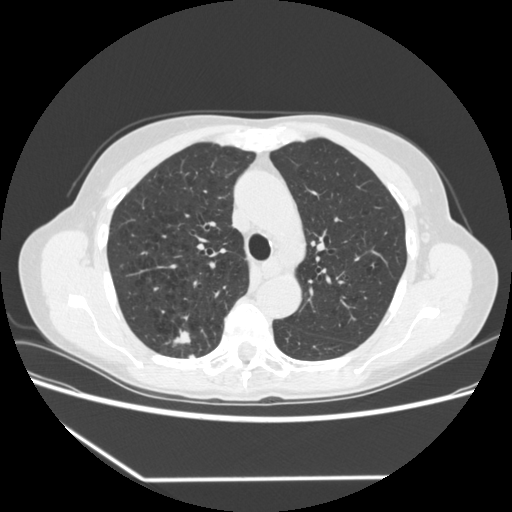
Low-dose screening chest CT, axial slice; baseline annual screen; lung window (W 1500 / L -600 HU); standard (soft-tissue) reconstruction kernel (STANDARD); 512 × 512 image matrix. Female participant, aged 67 years at enrolment. Current smoker at enrolment.
Expert-annotated lung lesion, bounding box <159,324,202,362> (left, top, right, bottom; pixels). The screening reader recorded 2 non-calcified nodules or masses ≥4 mm on this exam (right upper lobe, right lower lobe); which of them this box marks is not recorded. Official screen result: positive, change unspecified: nodule(s) >= 4 mm or enlarging nodule(s), mass(es), or other non-specific abnormalities suspicious for lung cancer.